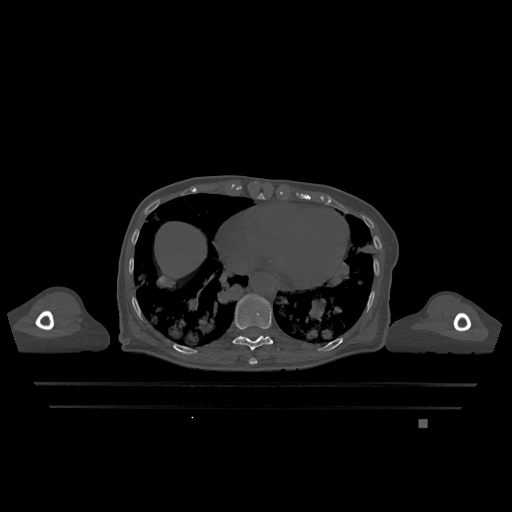
CT including the spine, one axial slice; slice 639 of 1317 in the series (ordered by position); bone window (W 1800 / L 400 HU); 512 × 512 image matrix, field of view 500 × 500 mm. Patient: female, 74 years. From the clinical record (not read from this slice): primary cancer: lung; vertebrae with lytic lesions (as recorded): T1, T4, T5, T6, L4, L5.
Outlined on this slice (semi-automatic segmentation, software-assisted and operator-edited):
- T10 vertebra: bounding box [x1, y1, x2, y2] px = [232, 294, 279, 351]
- T9 vertebra: [249, 358, 257, 365]